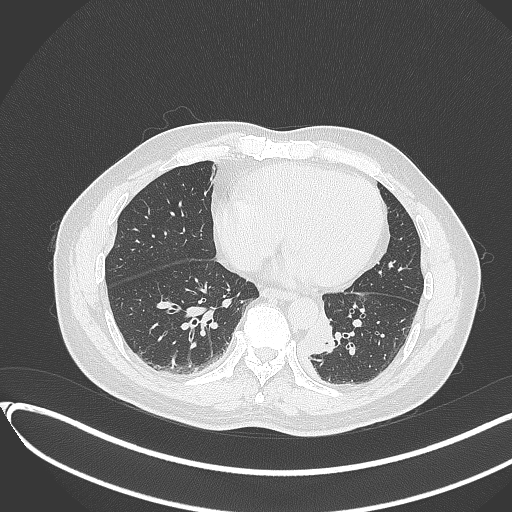
Chest CT, one axial slice; slice 114 of 417 in the series (ordered by position); reconstruction kernel B70f; lung window (W 1500 / L -600 HU); 512 × 512 image matrix, field of view 400 × 400 mm. Male patient, age 54 years. From the clinical record (not read from this slice): clinical TNM (as recorded): T3 N0 M0.
Outlined on this slice (bounding box drawn by a radiologist):
- lung tumour (recorded histology: squamous cell carcinoma): box from (x=301, y=310) to (x=337, y=355) px